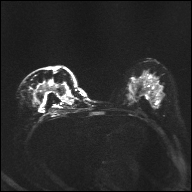
Breast MRI, one axial slice. Position 19 of 32 along the scan axis. Diffusion-weighted series; image 2 of 4 stored at this slice position (different b-values; order by instance number). 1.5 T. 192 × 192 image matrix. Female patient.
Outlined on this slice (outlined manually by an expert reader):
- tumour on diffusion-weighted imaging: bounding box (x1, y1, x2, y2) in pixels: (41, 84, 60, 91)